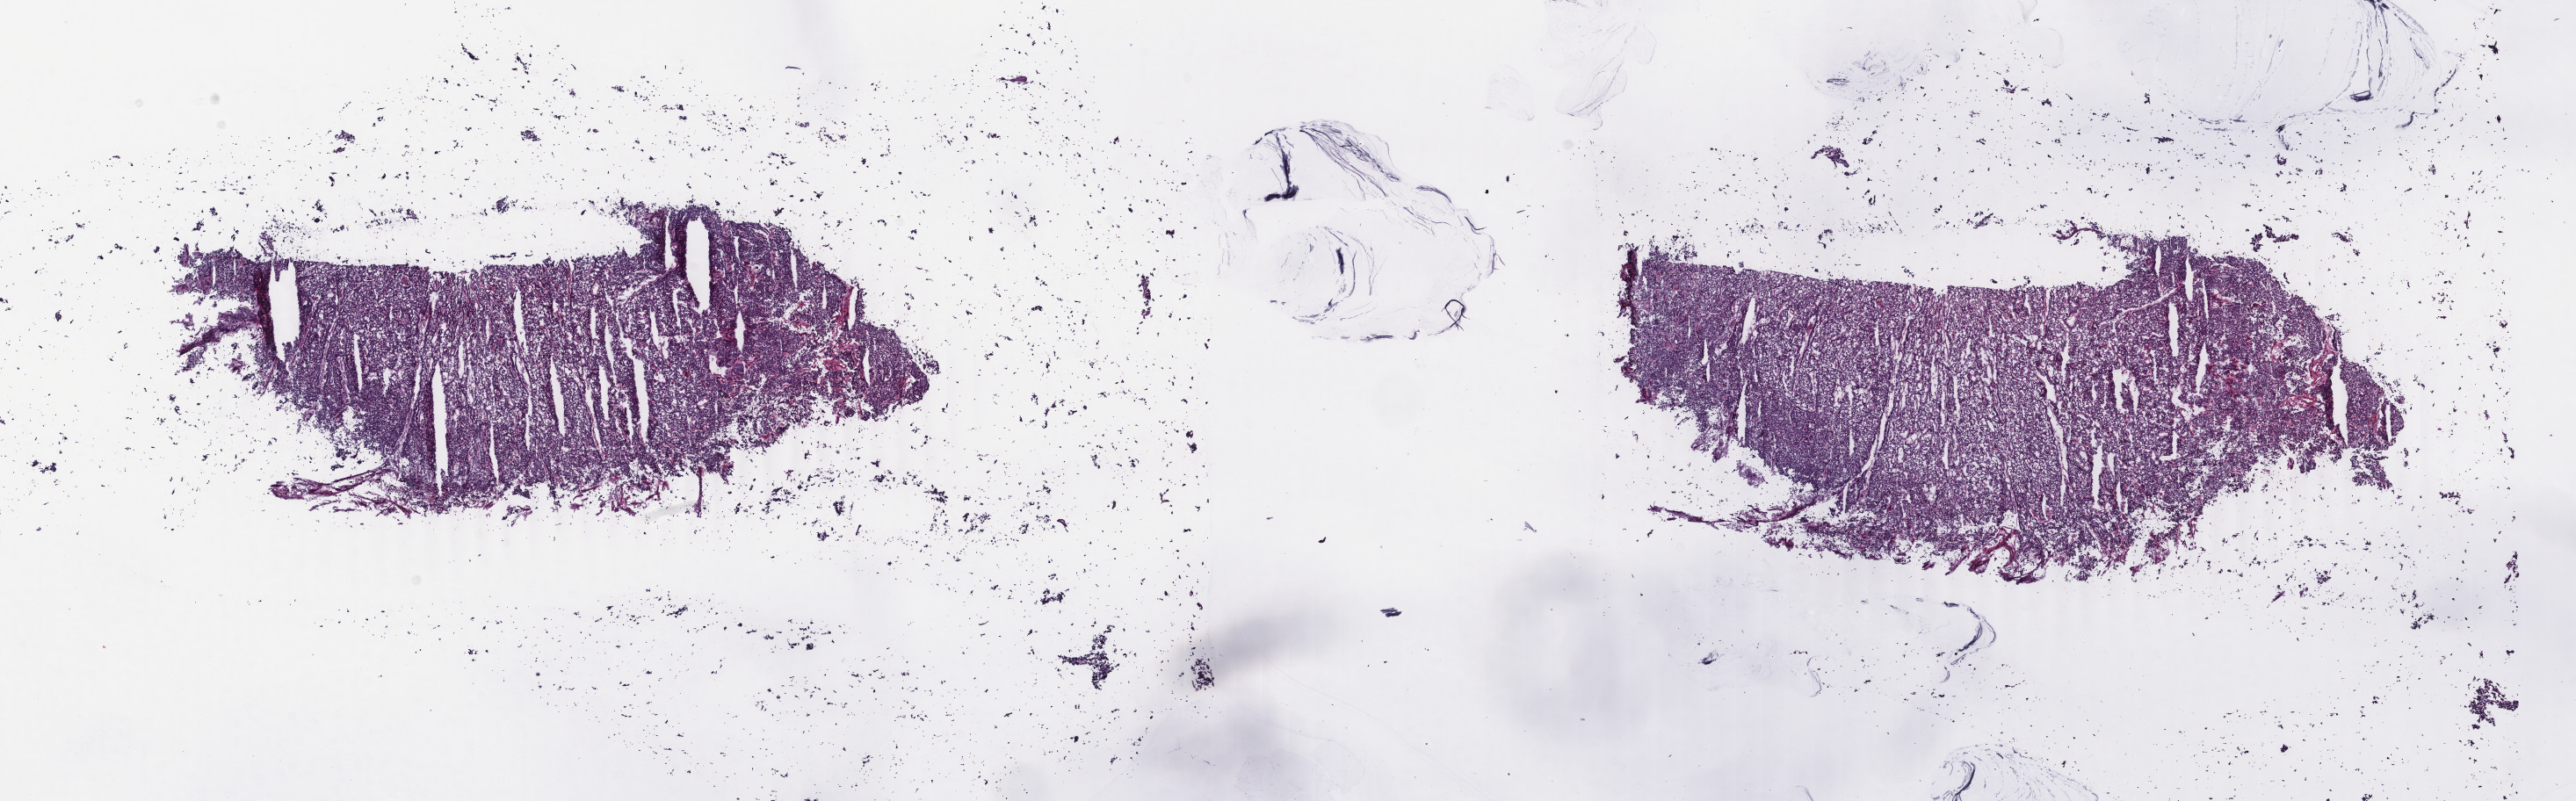
Whole-slide histology image, H&E-stained — a low-resolution overview of the entire scanned area, about 23.3 x 7.3 mm (slide scanned at 40x); frozen section from the top of the tissue portion; sample: primary tumour, thyroid. Female, age 49 years at initial diagnosis. Slide review estimates, as recorded: tumour cells 95%, tumour nuclei 95%, normal cells 0%, stromal cells 5%, necrosis 0%. Infiltration values recorded for this section: lymphocyte infiltration 1%, monocyte infiltration 0%, neutrophil infiltration 0%.
* lymph nodes positive (case pathology): 0 of 3 examined
* histologic diagnosis: Papillary carcinoma, columnar cell
* AJCC pathologic stage: I
* laterality: left